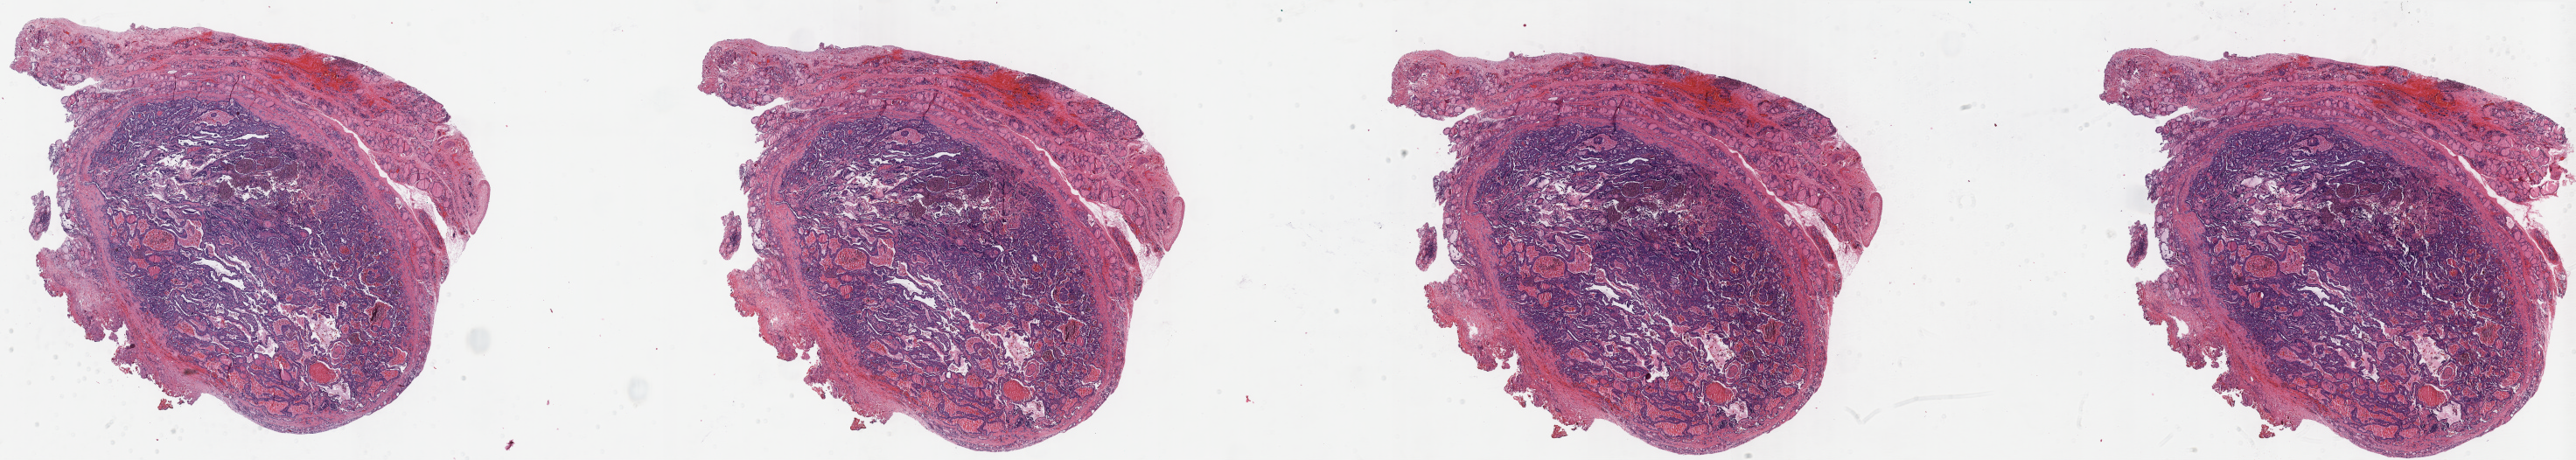
H&E-stained whole-slide image — shown as a low-resolution overview of the whole scanned area (about 46.4 x 8.3 mm, slide scanned at 40x); formalin-fixed paraffin-embedded (FFPE) diagnostic section; sample: primary tumour, thyroid. Female, age 46 years at initial diagnosis.
Diagnosis: Papillary adenocarcinoma, NOS (thyroid gland). Lymph nodes positive (case pathology): 0 of 4 examined. Laterality: right. AJCC pathologic stage: I.